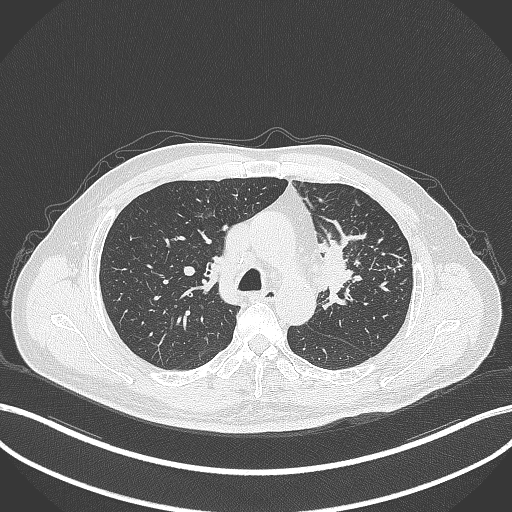
Chest CT, one axial slice; slice 239 of 386 in the series (ordered by position); reconstruction kernel B70f; 120 kVp; lung window (W 1500 / L -600 HU); 512 × 512 image matrix, field of view 400 × 400 mm. Patient: male, 69 years. From the clinical record (not read from this slice): clinical TNM (as recorded): T2a N2 M0.
Annotated regions visible in this slice (rectangle marked by the reading radiologist):
- lung tumour (recorded histology: adenocarcinoma): bounding box <315,232,358,314> (left, top, right, bottom; pixels)